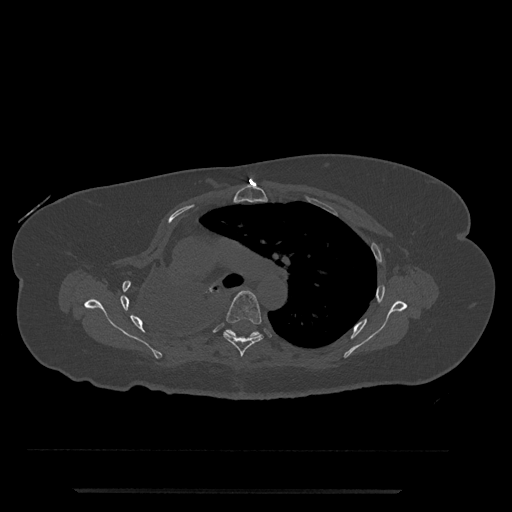
CT including the spine, one axial slice. Reconstruction kernel Br40s/3. 120 kVp. Bone window (W 1800 / L 400 HU). 0.5 mm slice thickness. 512 × 512 image matrix, field of view 440 × 440 mm. Female patient, age 51 years. Case-level facts recorded for this patient, not image findings: primary cancer: neuro; vertebrae with lytic lesions (as recorded): T8.
Structures marked on this image (semi-automatically segmented with operator editing):
- T5 vertebra: bounding box <223,290,263,357> (left, top, right, bottom; pixels)
- T6 vertebra: <224,329,261,338>